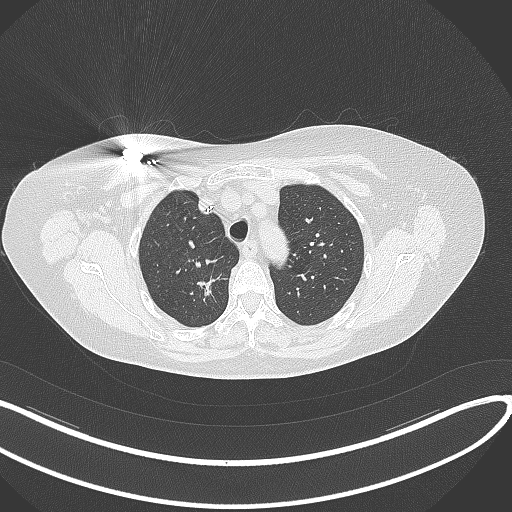
Chest CT, one axial slice; slice 263 of 316 in the series (ordered by position); lung window (W 1500 / L -600 HU); 512 × 512 image matrix, field of view 400 × 400 mm. Female patient, age 72 years. Case-level facts recorded for this patient, not image findings: clinical TNM (as recorded): T1c N0 M0.
Outlined on this slice (bounding box drawn by a radiologist):
- lung tumour (recorded histology: adenocarcinoma): bounding box [x1, y1, x2, y2] px = [194, 276, 225, 304]